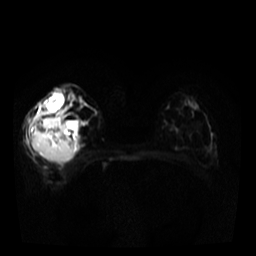
Breast MRI, one axial slice; position 17 of 34 along the scan axis; diffusion-weighted series; image 2 of 4 stored at this slice position (different b-values; order by instance number); 3 T; 5 mm slice thickness; 256 × 256 image matrix, field of view 320 × 320 mm. Female patient.
Outlined on this slice (outlined manually by an expert reader):
- tumour on diffusion-weighted imaging: bounding box [x1, y1, x2, y2] px = [32, 117, 76, 163]